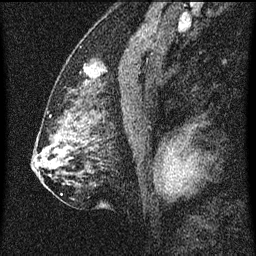
Breast MRI (dynamic contrast-enhanced), one sagittal slice. Position 36 of 60 along the scan axis. Dynamic contrast-enhanced series, image 2 of 3 at this slice position (ordered by acquisition). 1.5 T. TE 4.2 ms, TR 8 ms. 256 × 256 image matrix, field of view 180 × 180 mm. Patient: female, 52 years.
Outlined on this slice (semi-automatically segmented with operator editing):
- analysis volume of interest (the breast-tissue region the enhancement analysis was run in; not a lesion): bounding box <72,50,113,101> (left, top, right, bottom; pixels)
- tumour enhancement mask (voxels above the 70 % enhancement threshold inside the analysis volume of interest): <84,68,90,85>